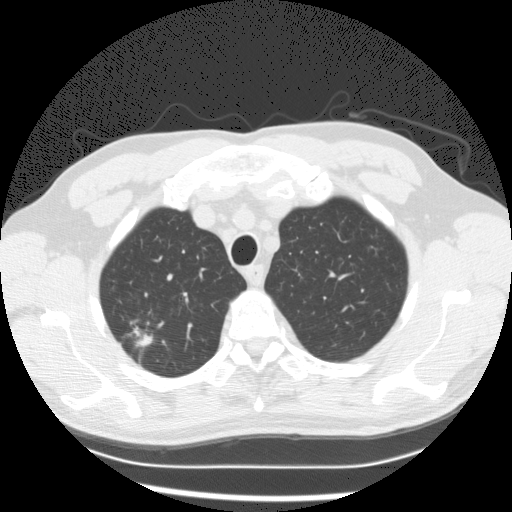
Low-dose screening chest CT, axial slice; baseline annual screen; lung window (W 1500 / L -600 HU); standard (soft-tissue) reconstruction kernel (STANDARD); slice 24 of 132 in the series; 512 × 512 image matrix. Male participant, aged 63 years at enrolment. Current smoker at enrolment.
Expert-annotated lung lesion, bounding box [x1, y1, x2, y2] px = [103, 306, 169, 365]. Screening reader's record for this exam (one nodule recorded; not confirmed to be the boxed lesion): non-calcified nodule or mass ≥4 mm, right upper lobe, 19 × 9 mm, poorly defined margins, mixed attenuation. Official screen result: positive, change unspecified: nodule(s) >= 4 mm or enlarging nodule(s), mass(es), or other non-specific abnormalities suspicious for lung cancer. Later outcome: lung cancer diagnosed 152 days after this screen — bronchiolo-alveolar adenocarcinoma, NOS, right upper lobe, moderately differentiated (G2), stage IA (AJCC 6th edition), 15 mm at pathology.